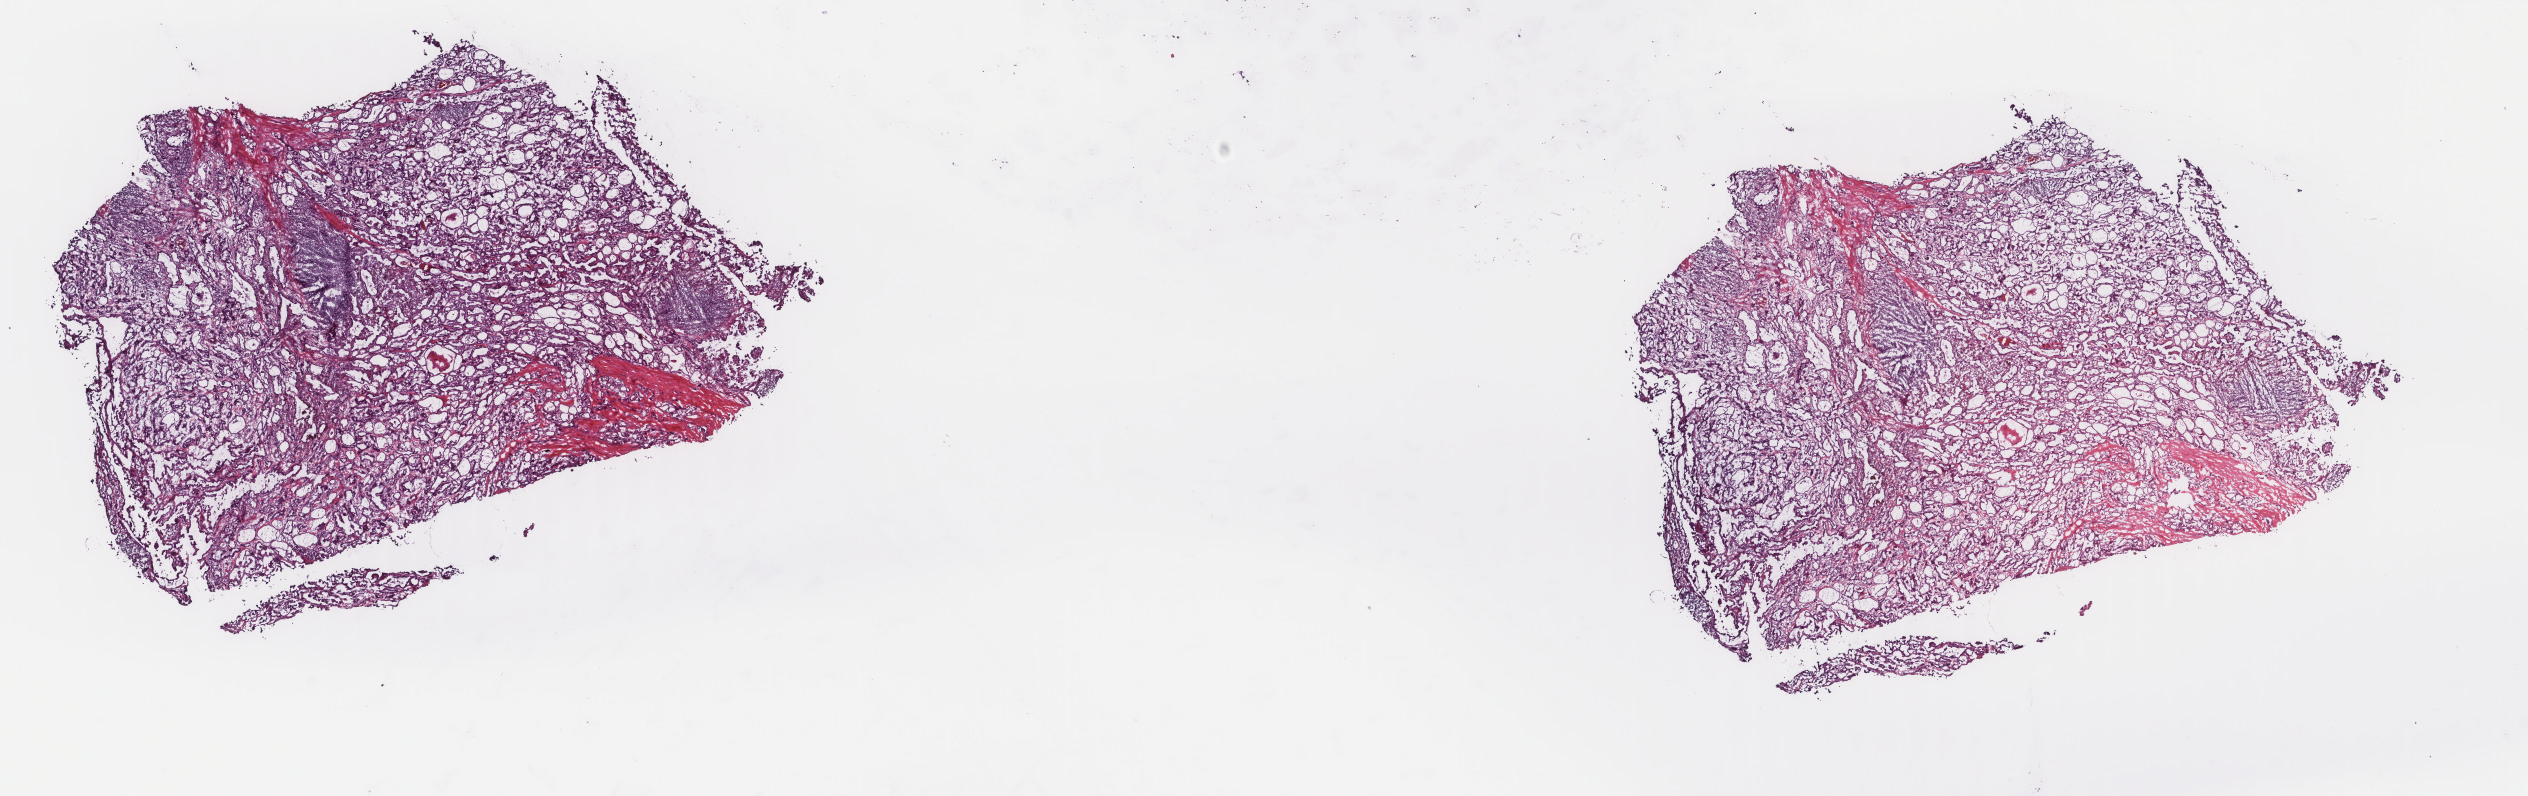
Digitized H&E tissue section (whole slide), shown as a low-resolution overview of the whole scanned area (about 20.1 x 6.3 mm); frozen section from the top of the tissue portion; thyroid, primary tumour sample. Patient: female, age at initial diagnosis 44 years. Composition of this section per pathologist review: tumour cells 100%, tumour nuclei 85%, normal cells 0%, stromal cells 0%, necrosis 0%. Infiltration values recorded for this section: lymphocyte infiltration 0%, monocyte infiltration 0%, neutrophil infiltration 0%.
TNM: T2 N1a M0. Lymph nodes positive (case pathology): 1 of 4 examined. Diagnosis: Papillary adenocarcinoma, NOS (thyroid gland). AJCC pathologic stage: I (7th edition).